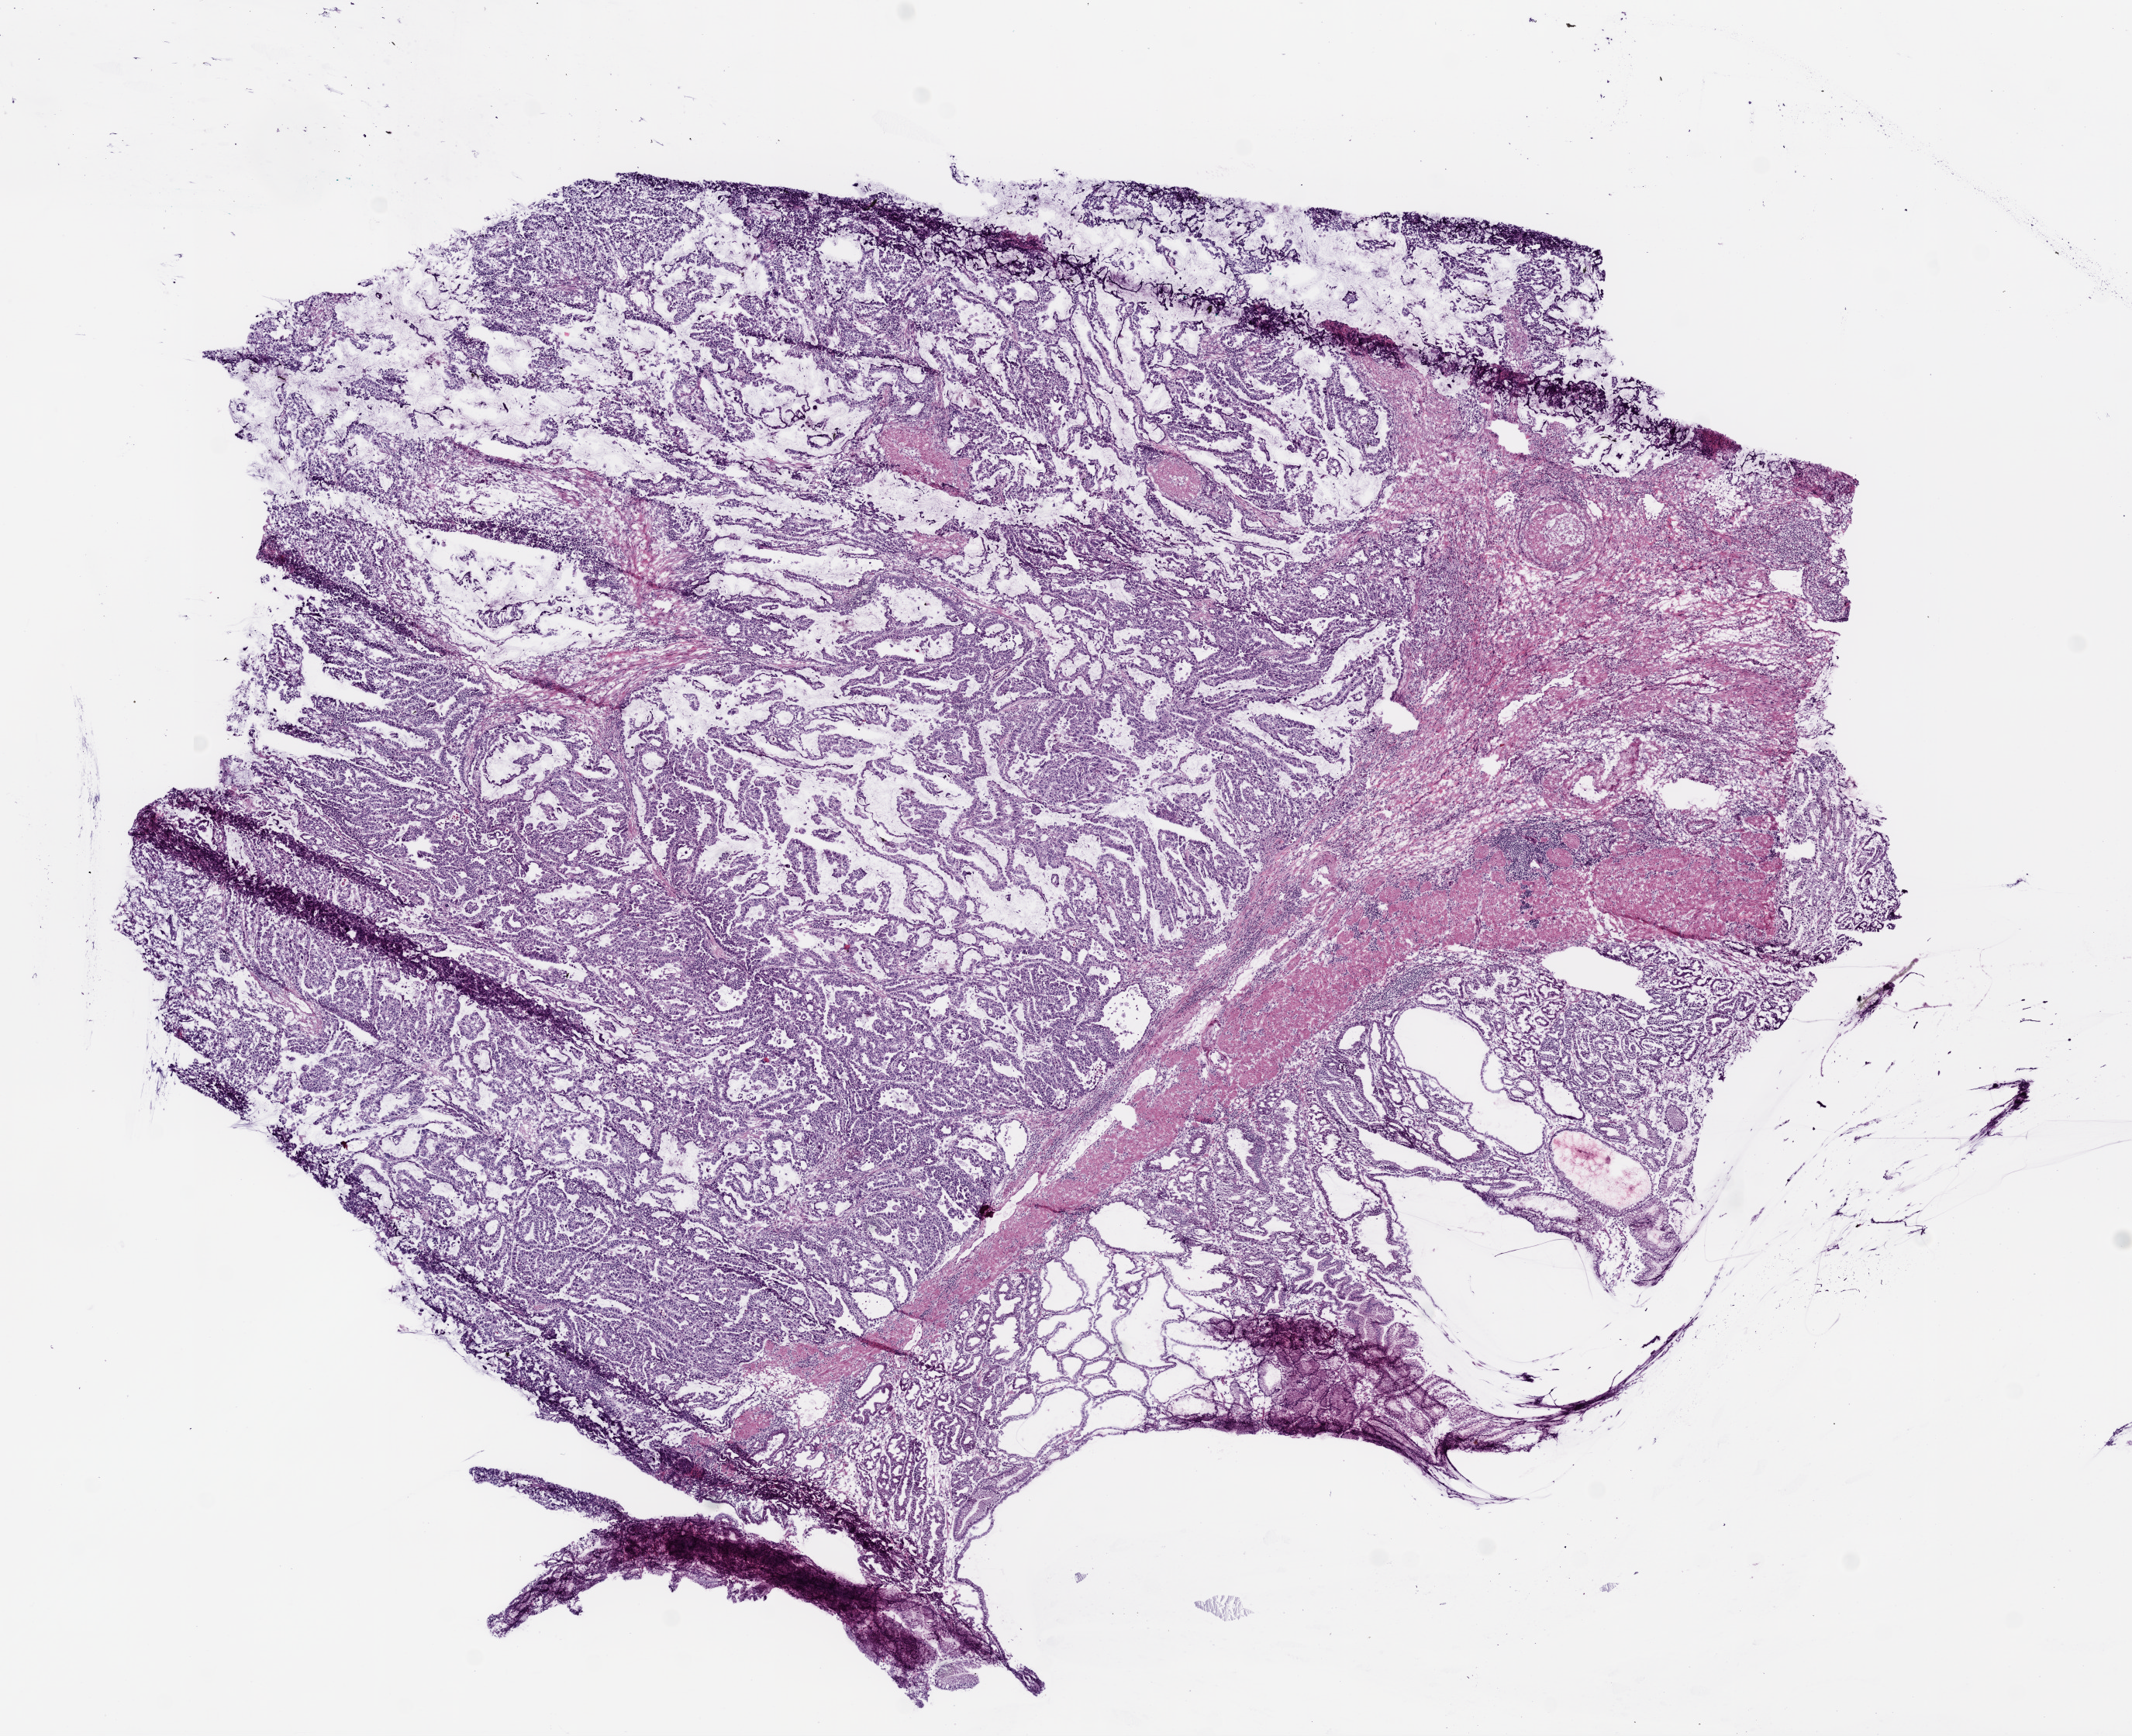
Digitized Hematoxylin and eosin (H&E) stained tissue section (whole slide) — a low-resolution overview of the entire scanned area, about 11.0 x 9.0 mm (from a 20x scan). Frozen section from the bottom of the tissue portion. Stomach, primary tumour sample. Patient: female, age at initial diagnosis 66 years. Histologic grade: G2 (moderately differentiated). Pathologist review of this section (percent, as recorded): tumour cells 60%, tumour nuclei 70%, normal cells 20%, stromal cells 10%, necrosis 10%.
Lymph nodes positive (case pathology): 2 of 33 examined. AJCC pathologic stage: IV (6th edition). Pathologic diagnosis: Adenocarcinoma, intestinal type (body of stomach).